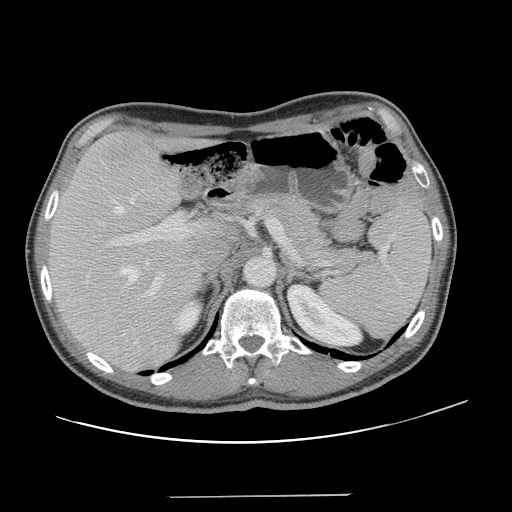
Contrast-enhanced abdominal CT, one axial slice; slice 88 of 131 in the series (ordered by position); 120 kVp; intravenous contrast given; soft-tissue window (W 400 / L 40 HU); 2.5 mm slice thickness; 512 × 512 image matrix, field of view 403 × 403 mm. Male patient, age 60 years. From the clinical record (not read from this slice): diagnosis: colorectal cancer liver metastases, imaged before liver resection.
Outlined on this slice (manually delineated by an expert):
- hepatic veins: box from (x=112, y=198) to (x=149, y=284) px
- liver: (x=48, y=131)–(x=206, y=370)
- planned liver remnant (the part of the liver to remain after resection): (x=49, y=131)–(x=217, y=355)
- portal vein (with intrahepatic branches): (x=99, y=214)–(x=202, y=295)